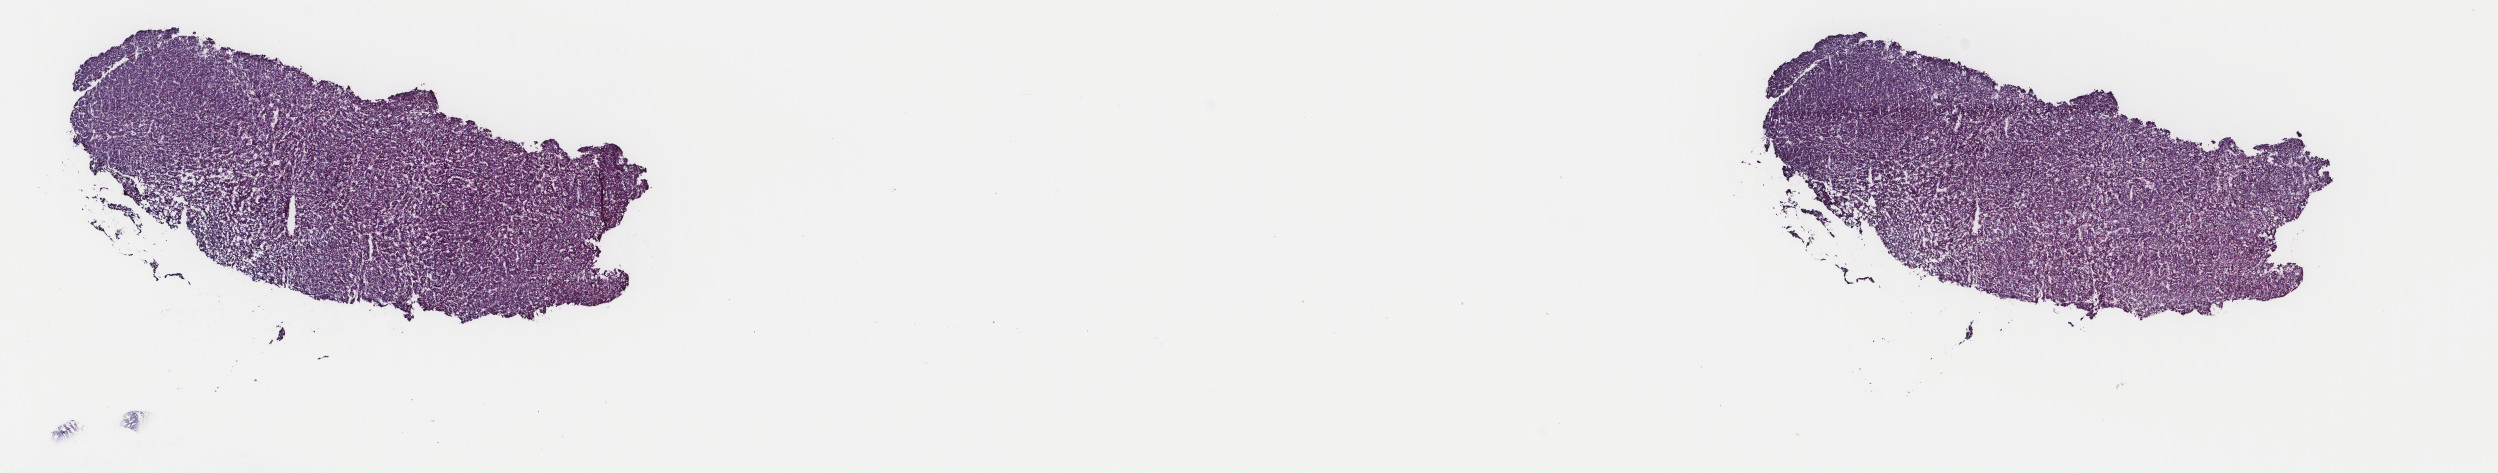
Digitized H&E tissue section (whole slide), whole scanned area (about 19.8 x 3.8 mm, acquisition: 40x scan) shown as a low-resolution overview, frozen section from the top of the tissue portion, sample: primary tumour, liver. Male, age 44 years at initial diagnosis. Histologic grade: G2 (moderately differentiated). Composition of this section per pathologist review: tumour cells 85%, tumour nuclei 94%, normal cells 0%, stromal cells 10%, necrosis 5%. Infiltration values recorded for this section: lymphocyte infiltration 3%, monocyte infiltration 0%, neutrophil infiltration 0%.
* AJCC pathologic stage: II
* histologic diagnosis: Hepatocellular carcinoma, NOS